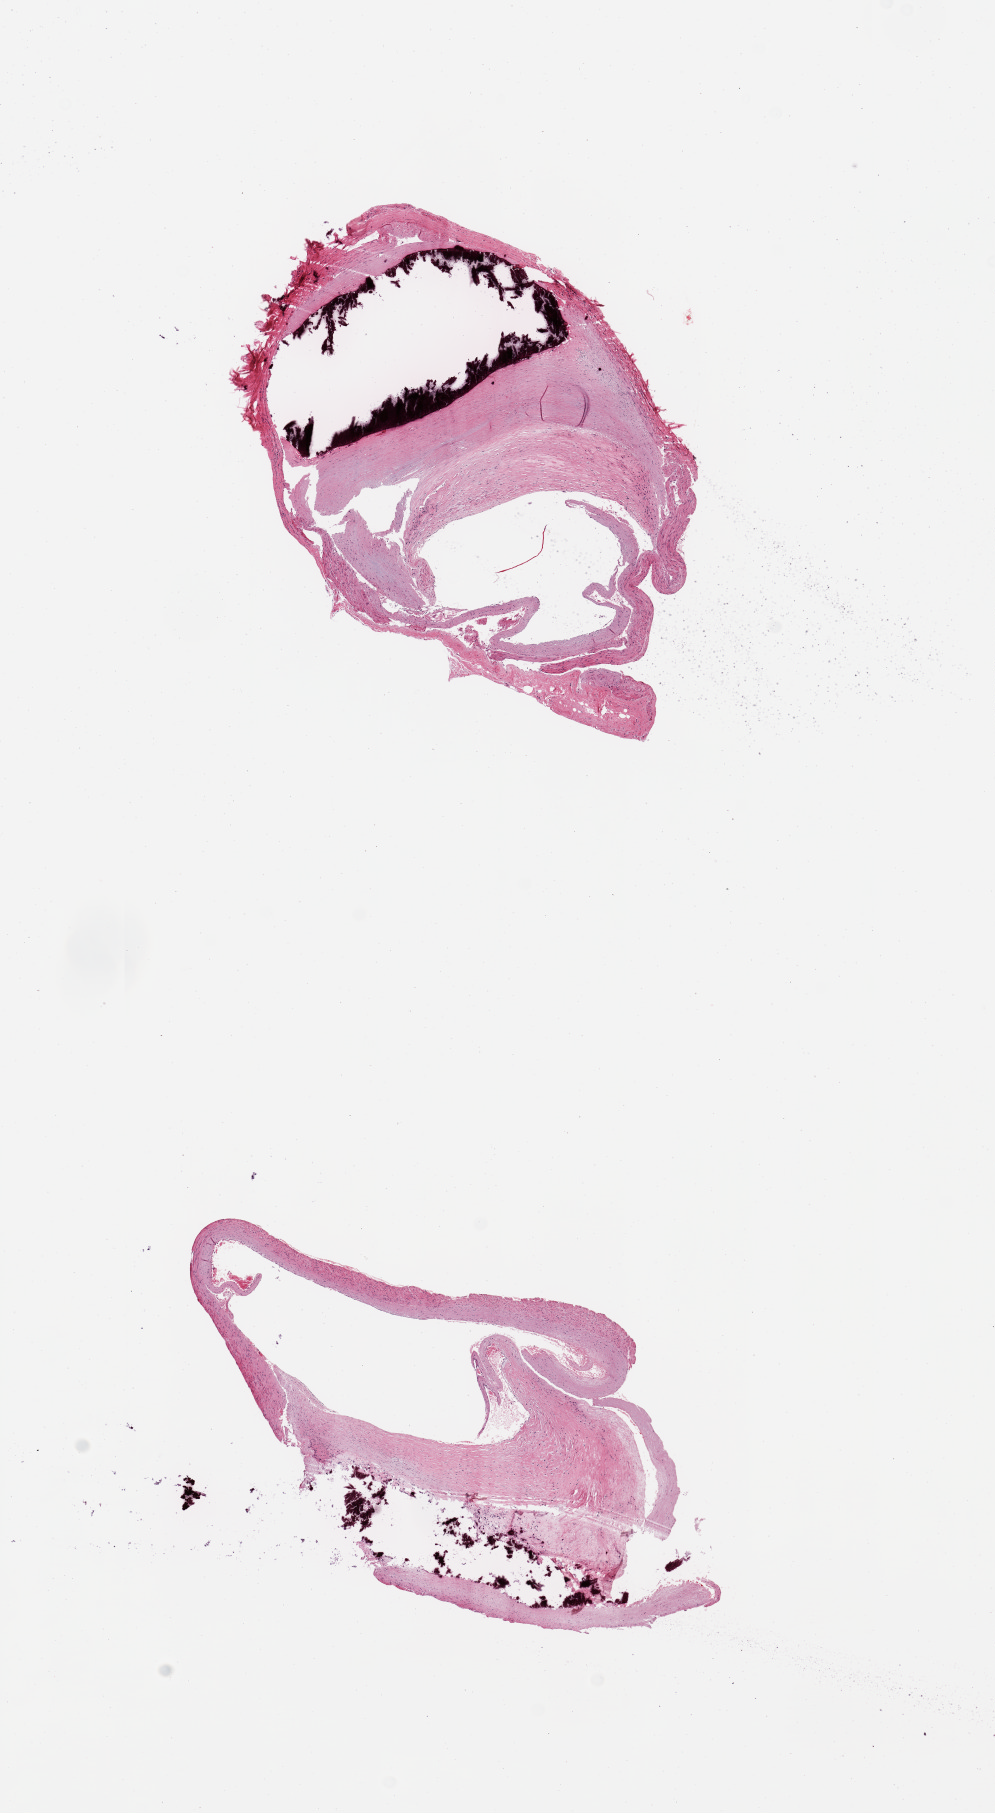
Whole-slide image, H&E stain — a low-resolution overview of the entire scanned area, about 7.9 x 14.3 mm, PAXgene-fixed paraffin-embedded (PFPE) section, sampled site (target tissue): coronary artery, donor tissue sample.
Pathologist's review note for this sample: 2 pieces; mild to moderated autolysis; eccentric atherosclerotic plaque and large calcification with 50% luminal compromise.